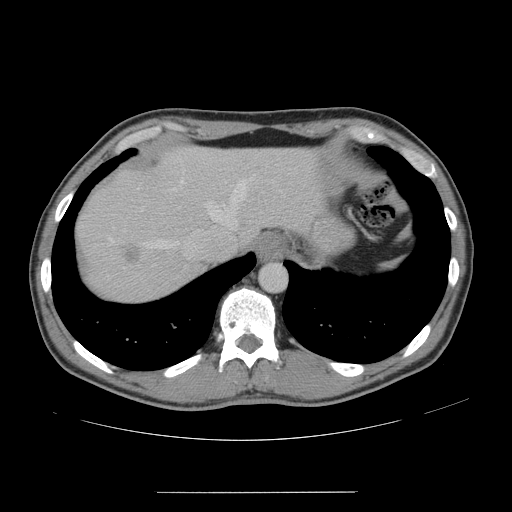
Contrast-enhanced abdominal CT, one axial slice. Position 128 of 178 along the scan axis. 120 kVp. Soft-tissue window (W 400 / L 40 HU). 2.5 mm slice thickness. 512 × 512 image matrix, field of view 401 × 401 mm. Male patient, age 53 years. Case-level facts recorded for this patient, not image findings: diagnosis: colorectal cancer liver metastases, imaged before liver resection; multiple liver metastases: yes; largest metastasis: 2.4 cm; disease in both lobes: no.
Outlined on this slice (outlined manually by an expert reader):
- hepatic veins: box from (x=110, y=180) to (x=248, y=256) px
- liver: (x=77, y=147)–(x=315, y=302)
- planned liver remnant (the part of the liver to remain after resection): (x=164, y=146)–(x=317, y=241)
- liver metastasis: (x=122, y=244)–(x=141, y=265)